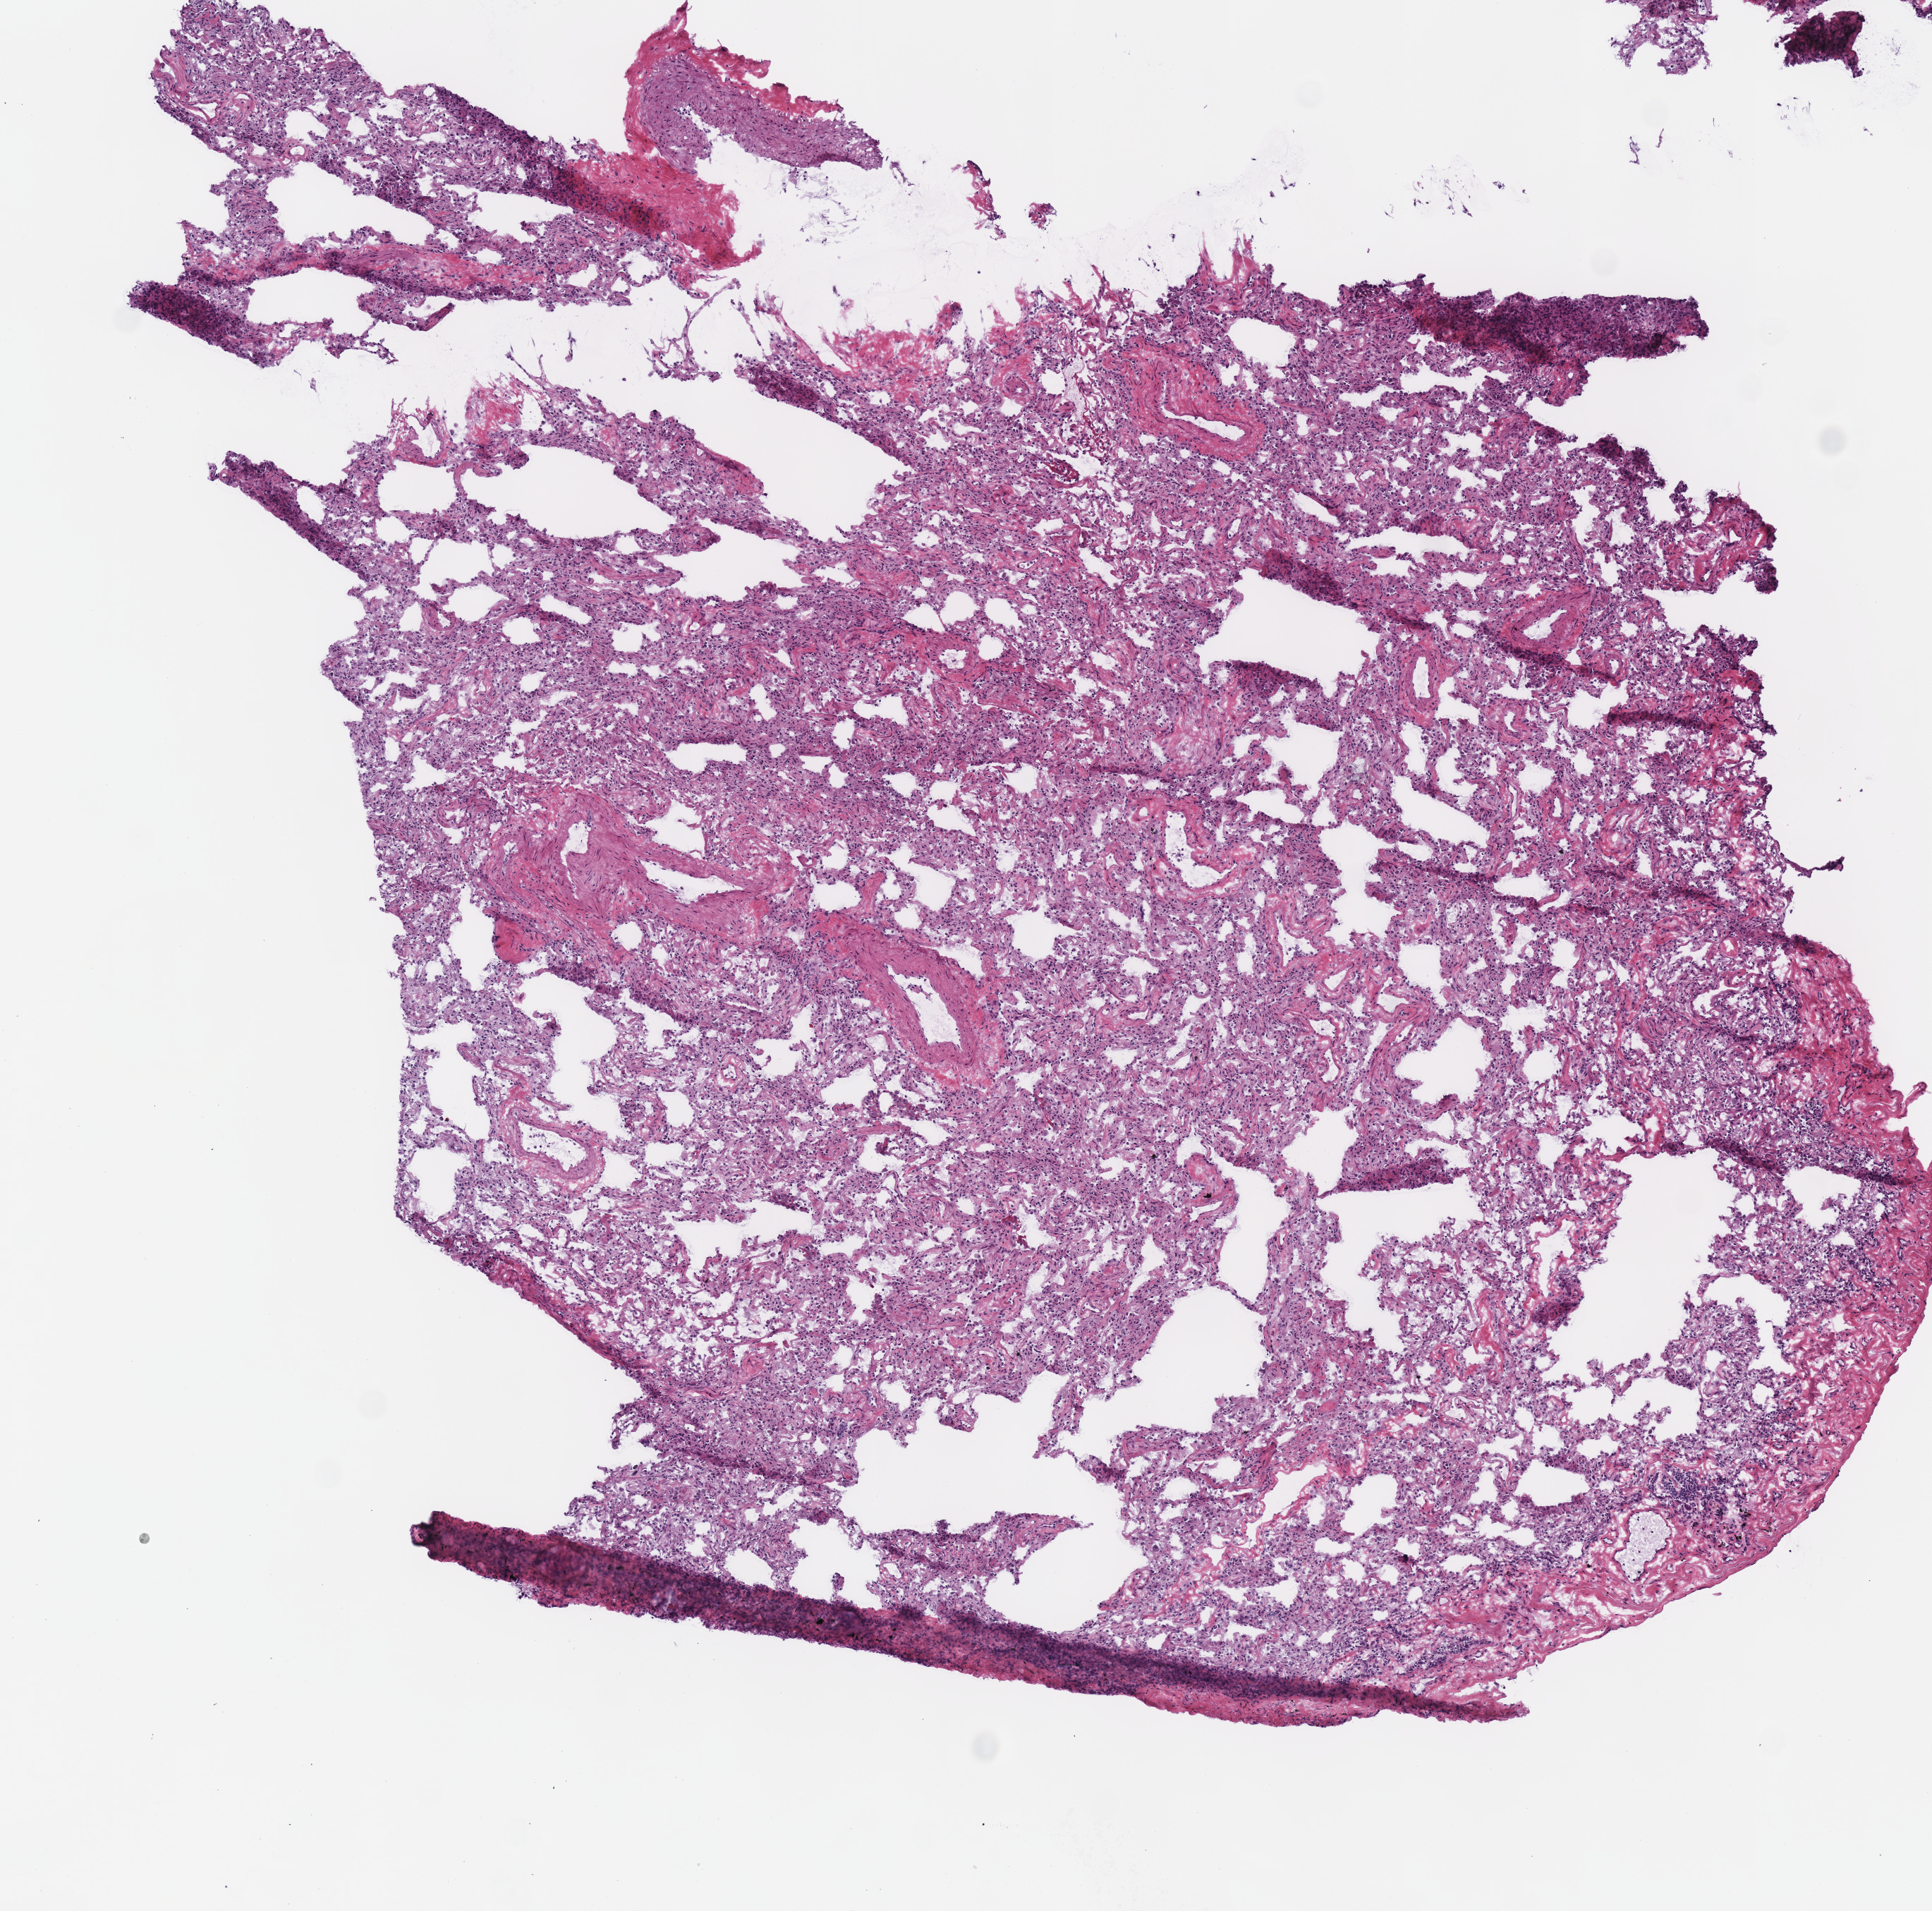
H&E whole-slide image — low-resolution overview of the scanned area, about 5.4 x 5.3 mm, frozen section from the top of the tissue portion, lung, solid tissue normal (non-tumour tissue) sample. Patient: male, age at initial diagnosis 70 years. Inflammatory infiltration, as recorded: lymphocyte infiltration 2%, monocyte infiltration 5%, neutrophil infiltration 0%.
This section: solid tissue normal sample (biorepository sample class). Patient diagnosis: Squamous cell carcinoma, NOS (lower lobe, lung).